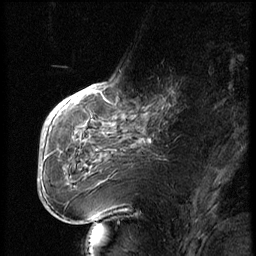
Breast MRI (dynamic contrast-enhanced), one sagittal slice. Slice 23 of 74 in the series (ordered by position). Dynamic contrast-enhanced series, image 2 of 3 at this slice position (ordered by acquisition). 1.5 T. TE 4.2 ms, TR 9 ms. 2.5 mm slice thickness. 256 × 256 image matrix, field of view 180 × 180 mm. Patient: female, 56 years. From the clinical record (not read from this slice): setting: breast cancer imaged before/during neoadjuvant chemotherapy.
Outlined on this slice (semi-automatically segmented with operator editing):
- analysis volume of interest (the breast-tissue region the enhancement analysis was run in; not a lesion): bounding box <123,71,195,131> (left, top, right, bottom; pixels)
- tumour enhancement mask (voxels above the 140 % enhancement threshold inside the analysis volume of interest): <143,88,174,114>